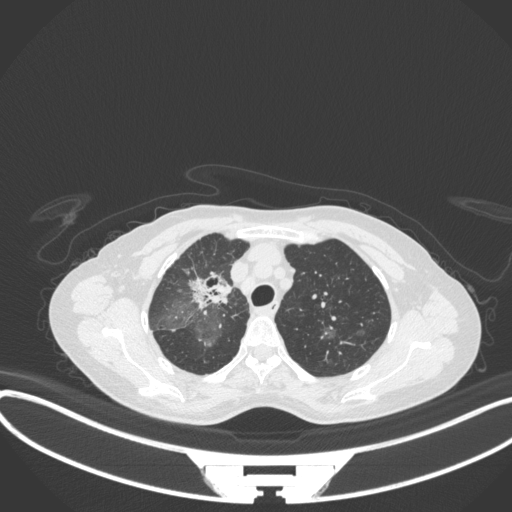
Chest CT, one axial slice. Slice 247 of 311 in the series (ordered by position). 120 kVp. Lung window (W 1500 / L -600 HU). 1 mm slice thickness. 512 × 512 image matrix, field of view 400 × 400 mm. Patient: female, 59 years. Case-level facts recorded for this patient, not image findings: clinical TNM (as recorded): T3 N0 M0.
Structures marked on this image (rectangle marked by the reading radiologist):
- lung tumour (recorded histology: adenocarcinoma): bounding box <189,266,233,309> (left, top, right, bottom; pixels)